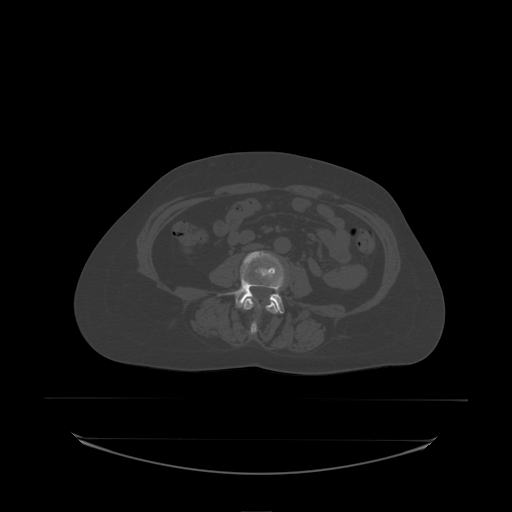
CT including the spine, one axial slice; position 54 of 242 along the scan axis; bone window (W 1800 / L 400 HU); 2.5 mm slice thickness; 512 × 512 image matrix, field of view 500 × 500 mm. Patient: female, 53 years. From the clinical record (not read from this slice): primary cancer: lung; vertebrae with lytic lesions (as recorded): T7, L1.
Annotated regions visible in this slice (semi-automatically segmented with operator editing):
- L3 vertebra: bounding box <244,298,278,335> (left, top, right, bottom; pixels)
- L4 vertebra: <219,251,285,314>